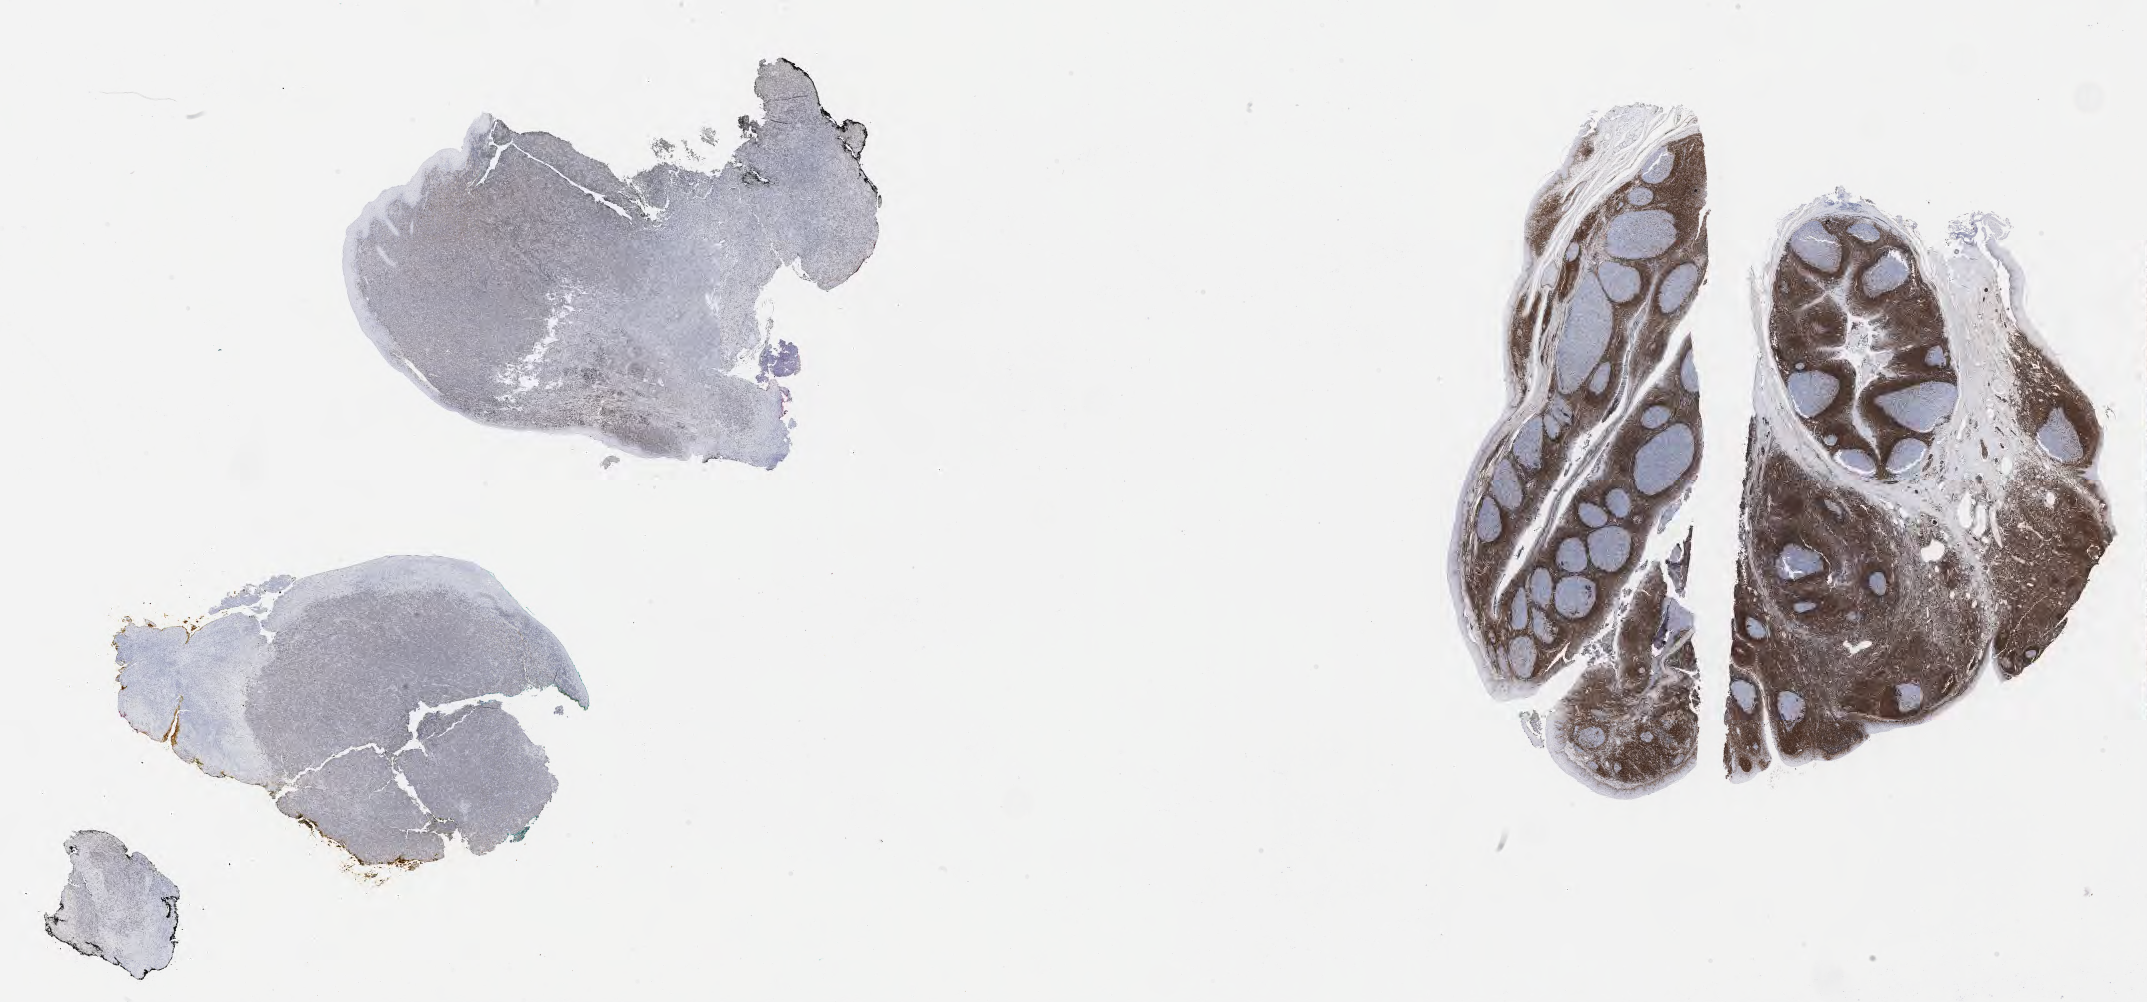
Whole-slide image, immunohistochemical stain for BCL2, a low-resolution overview of the entire scanned area, about 34.7 x 16.2 mm, specimen: tumor tissue. Patient: male, aged 49.
Diagnosis: Diffuse large B-cell lymphoma, NOS.